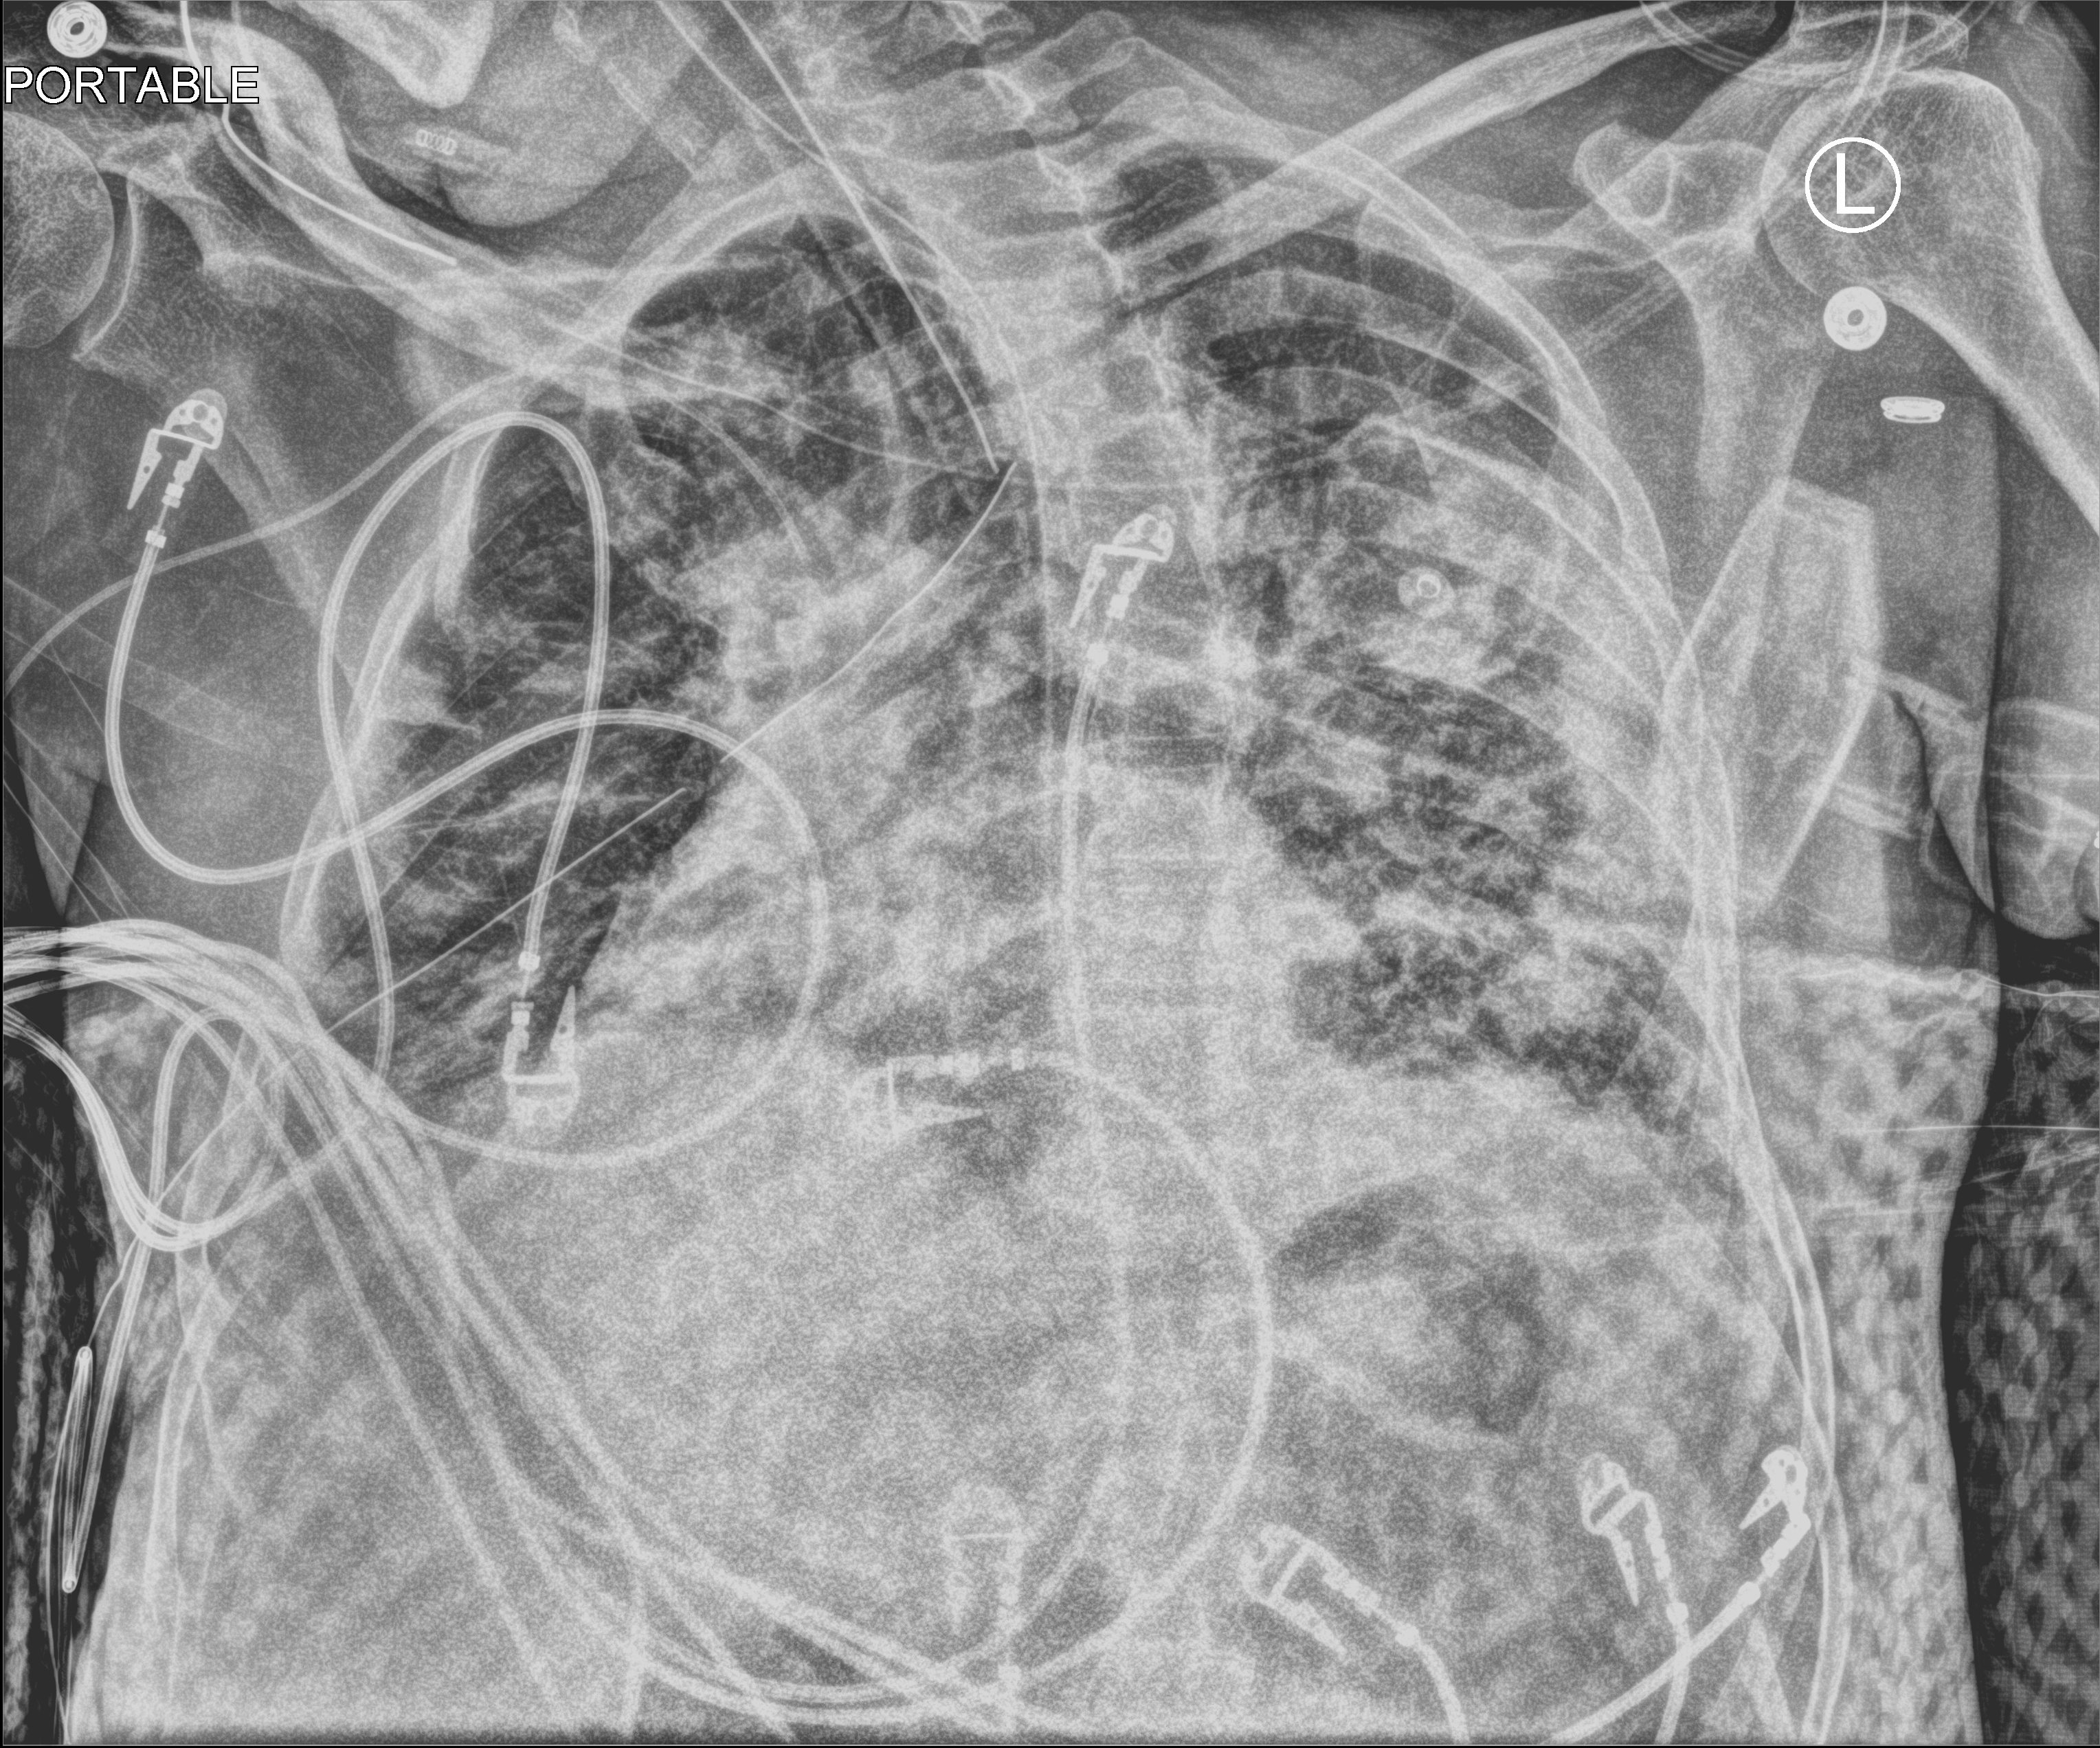
Chest X-ray (portable); anteroposterior (AP) projection. Patient hospitalised with COVID-19; male, aged 18–59 years.
Admission-level facts for this patient (not findings on this image; timing relative to this image not recorded): length of hospital stay: 41 days.